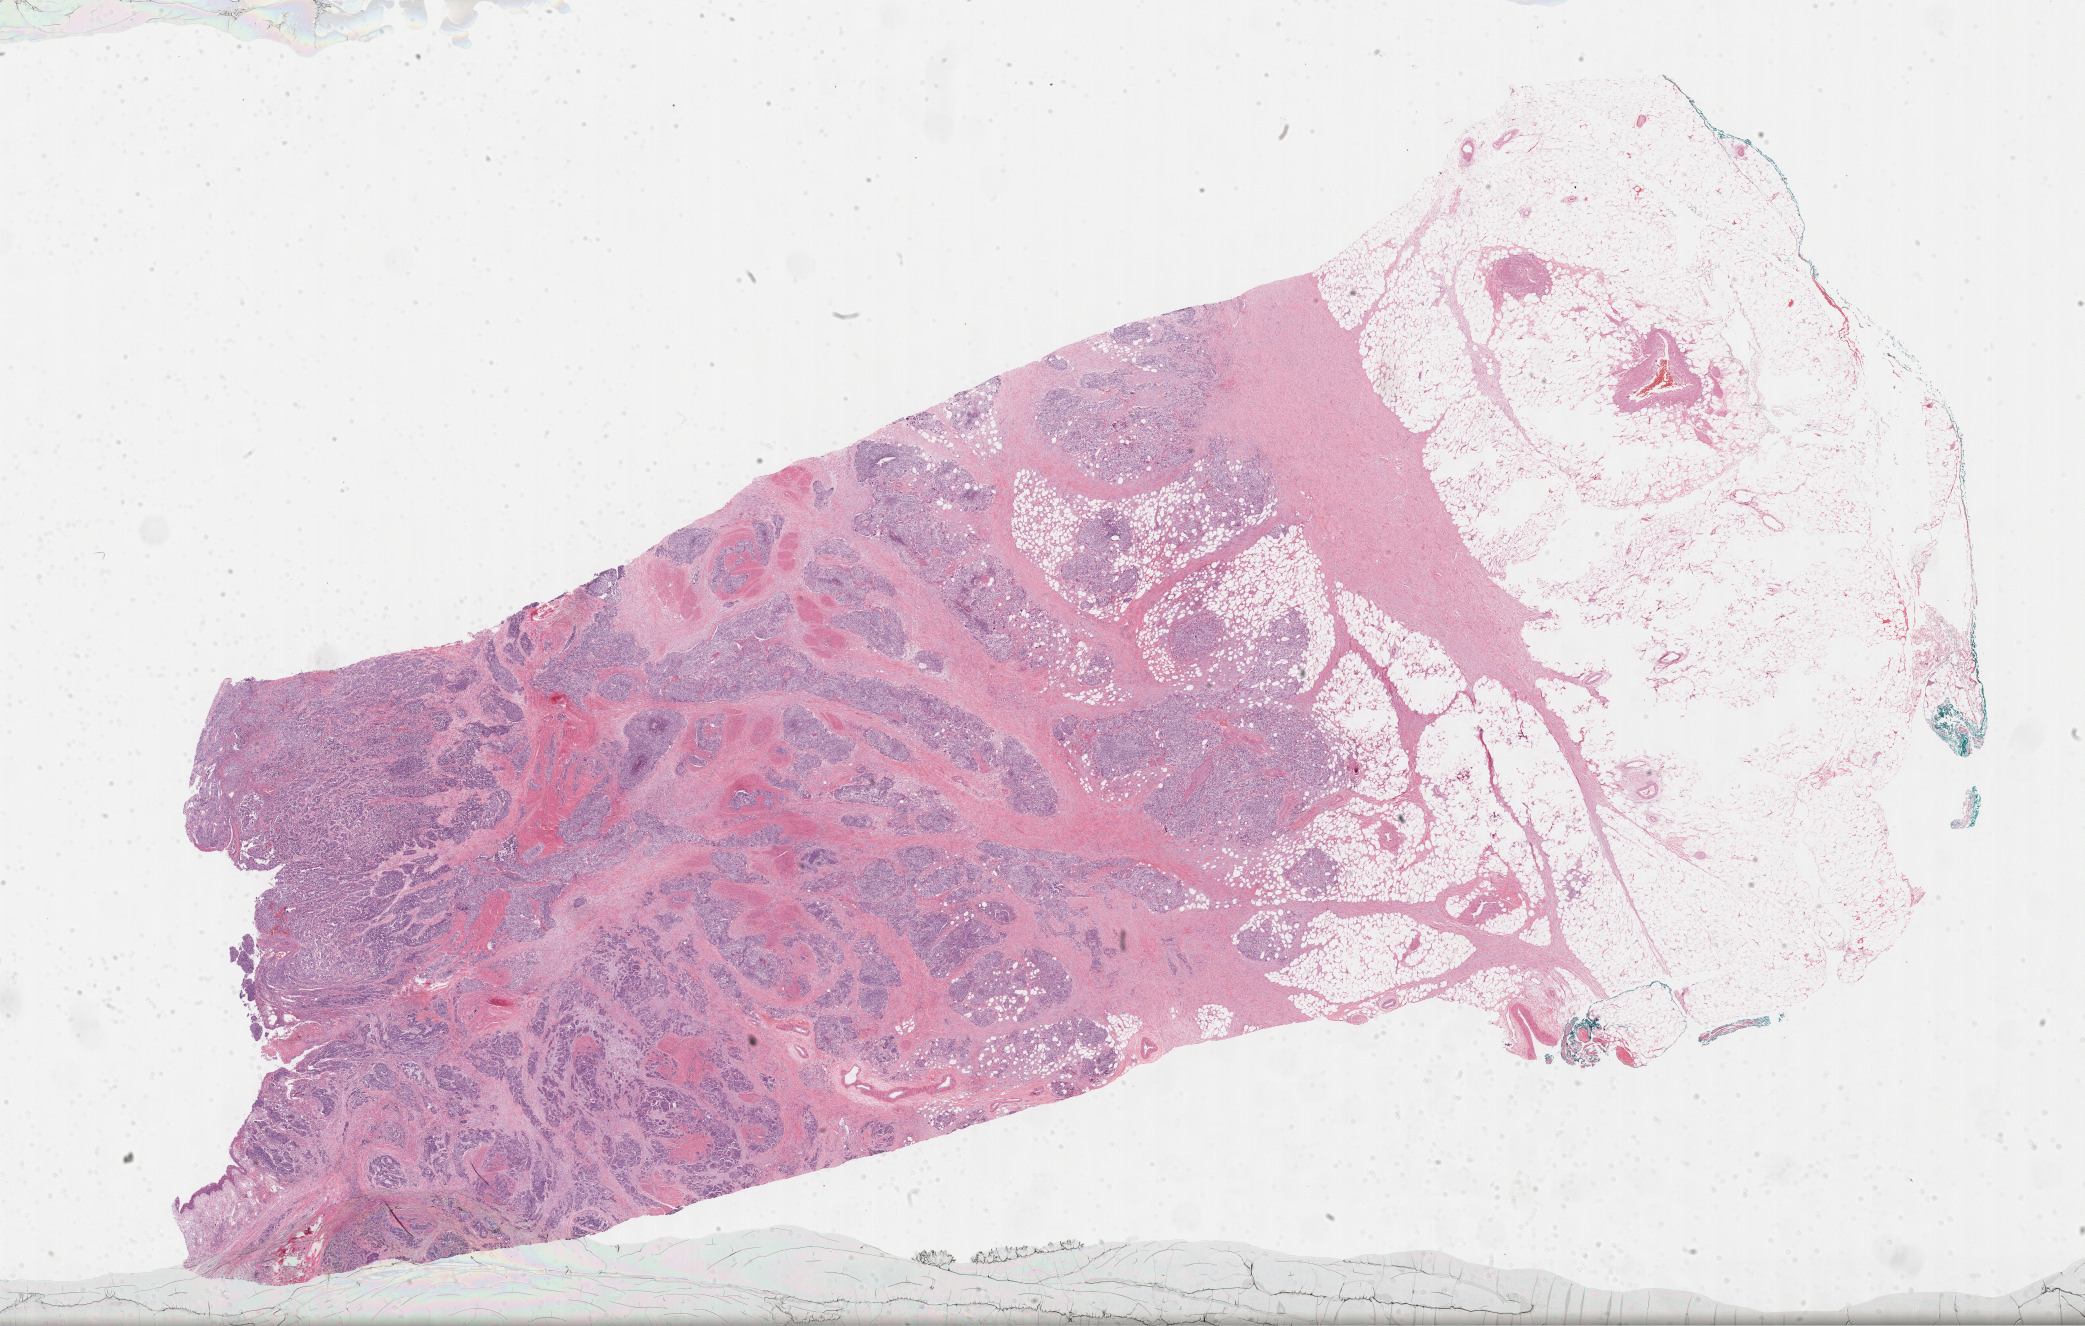
Digitized H&E-stained tissue section (whole slide) — shown as a low-resolution overview of the whole scanned area (about 33.7 x 21.4 mm, from a 40x scan); formalin-fixed paraffin-embedded (FFPE) diagnostic section; sample: primary tumour, bladder. Male, age 79 years at initial diagnosis. Histologic grade: high grade.
- lymph nodes positive (case pathology): 1 of 15 examined
- AJCC pathologic stage: IV (6th edition)
- diagnosis: Transitional cell carcinoma